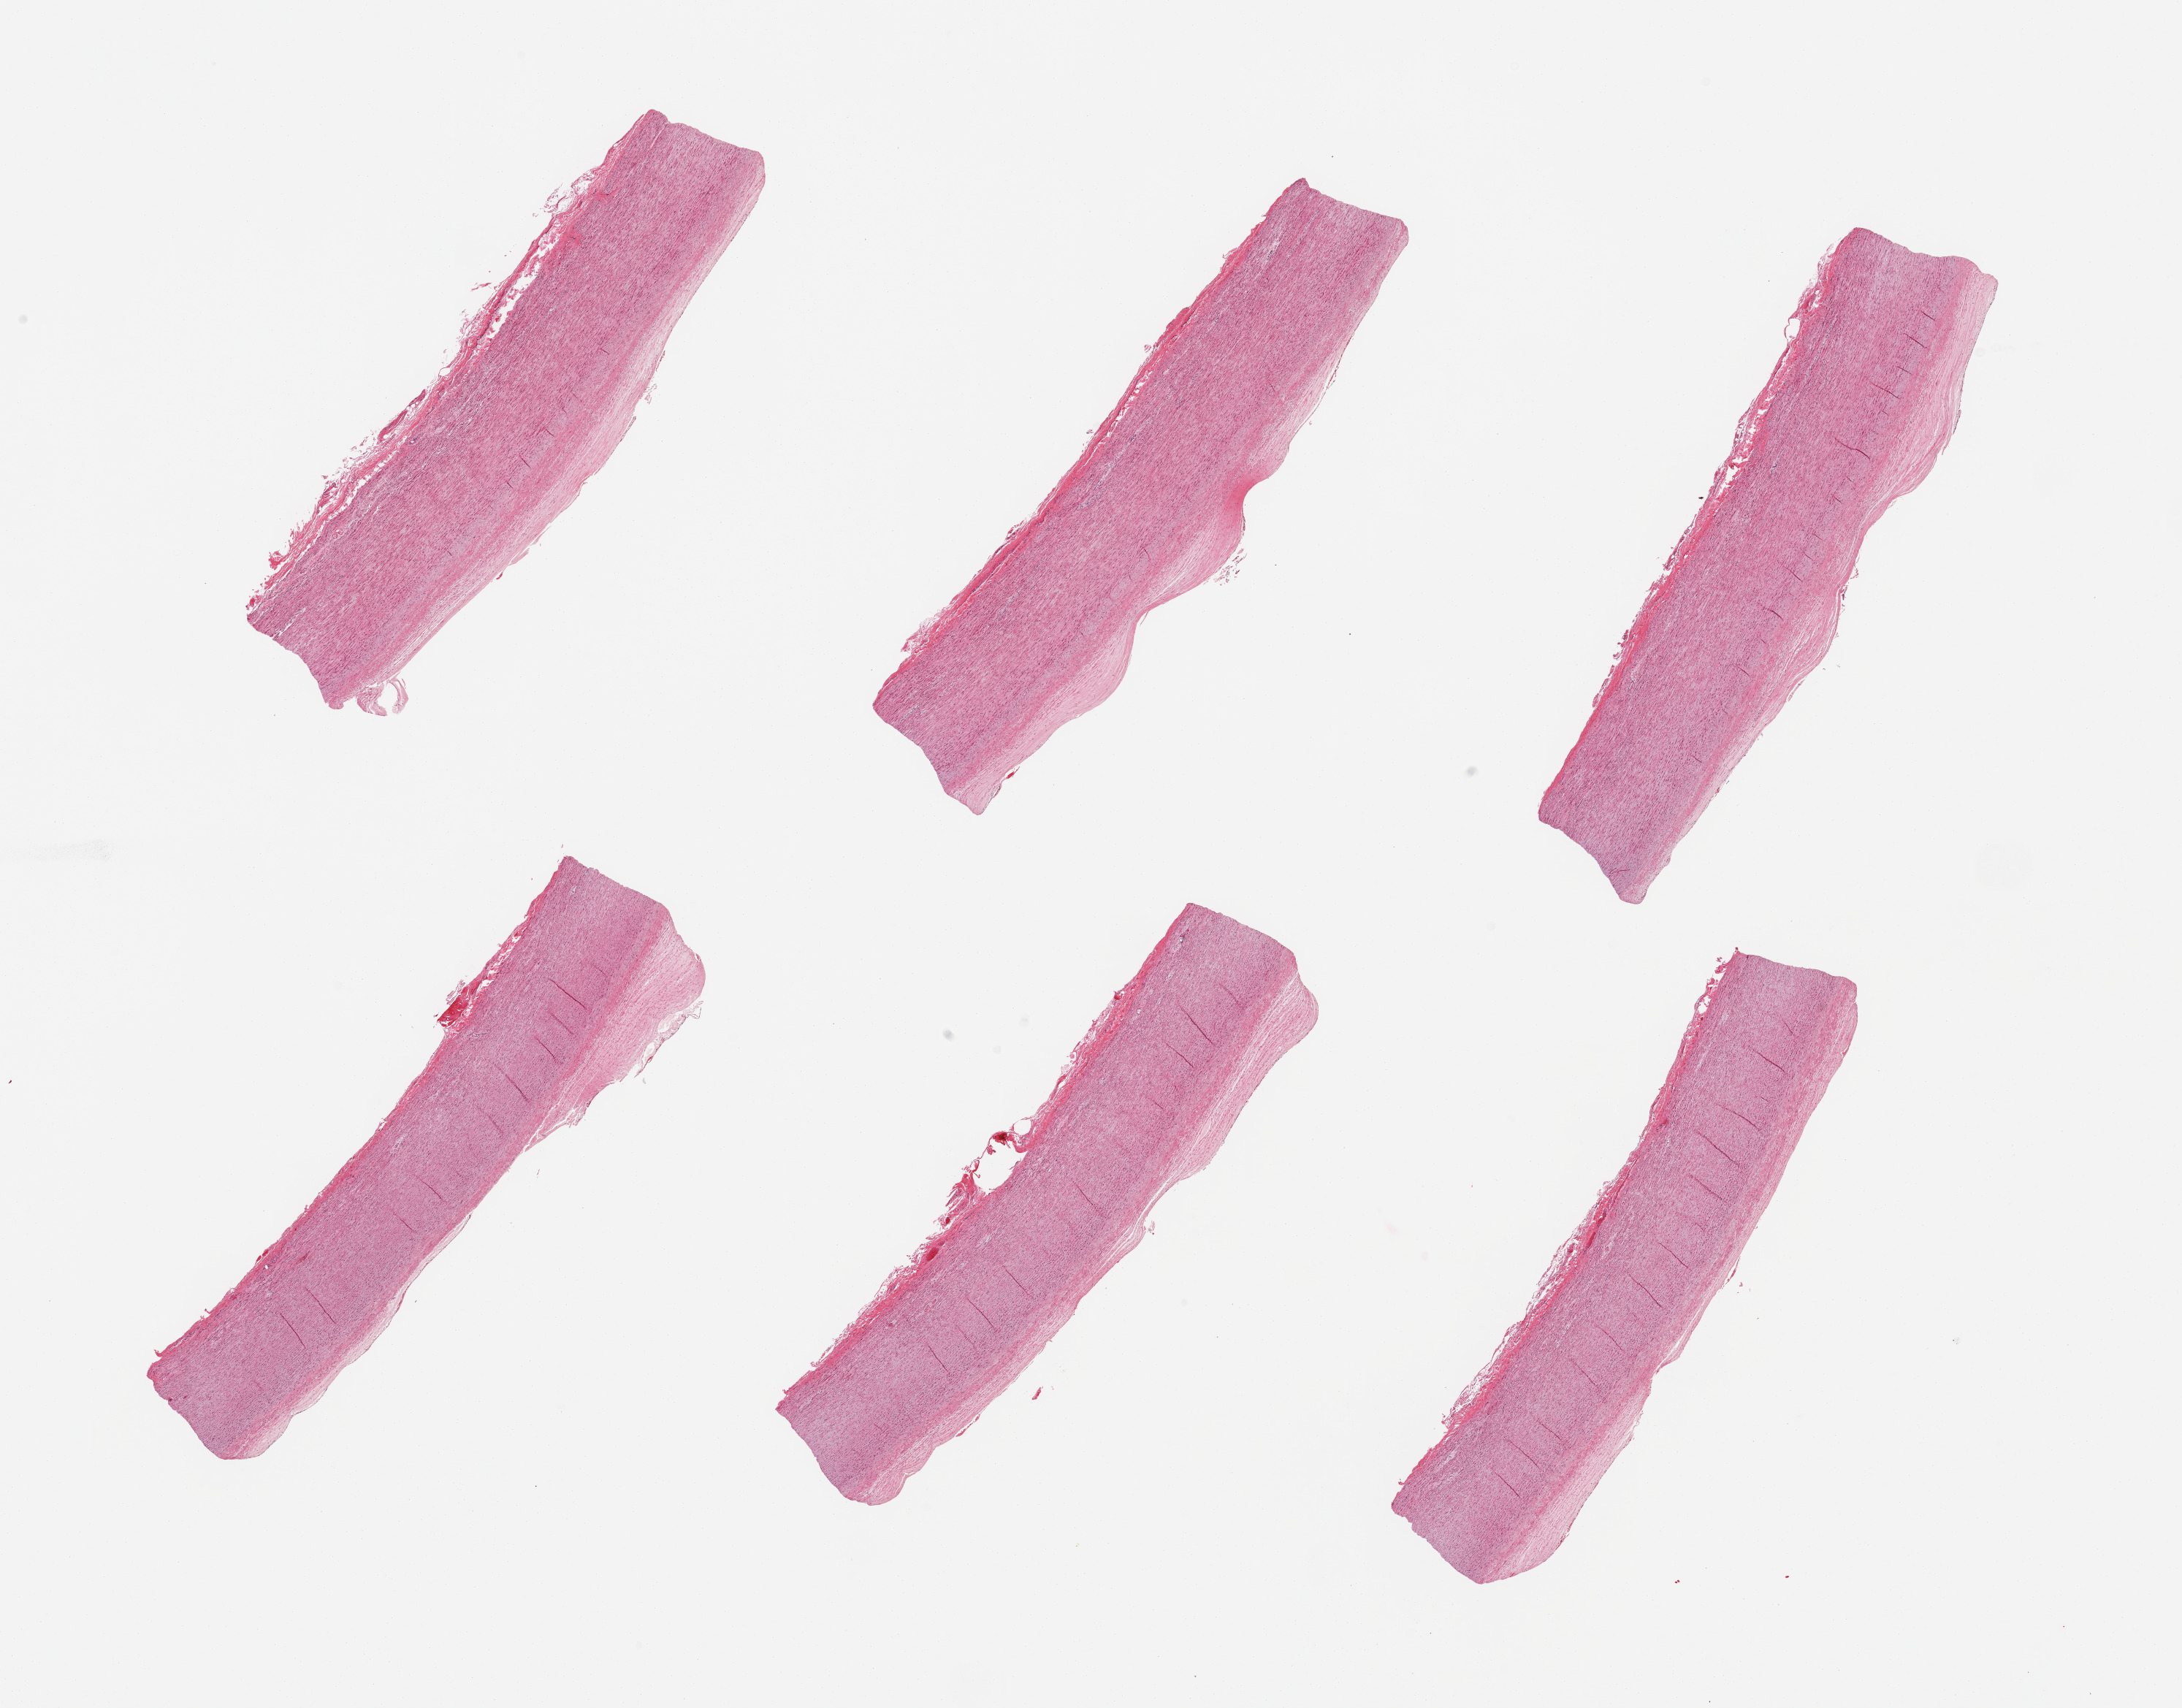
Whole-slide image, haematoxylin and eosin stain — shown as a low-resolution overview of the whole scanned area (about 23.6 x 18.5 mm); PAXgene-fixed paraffin-embedded (PFPE) section; sampled site (target tissue): aorta; tissue donor sample. Donor sex: female.
Reviewer comment on this tissue sample: 6pieces; thin plaques; well trimmed.